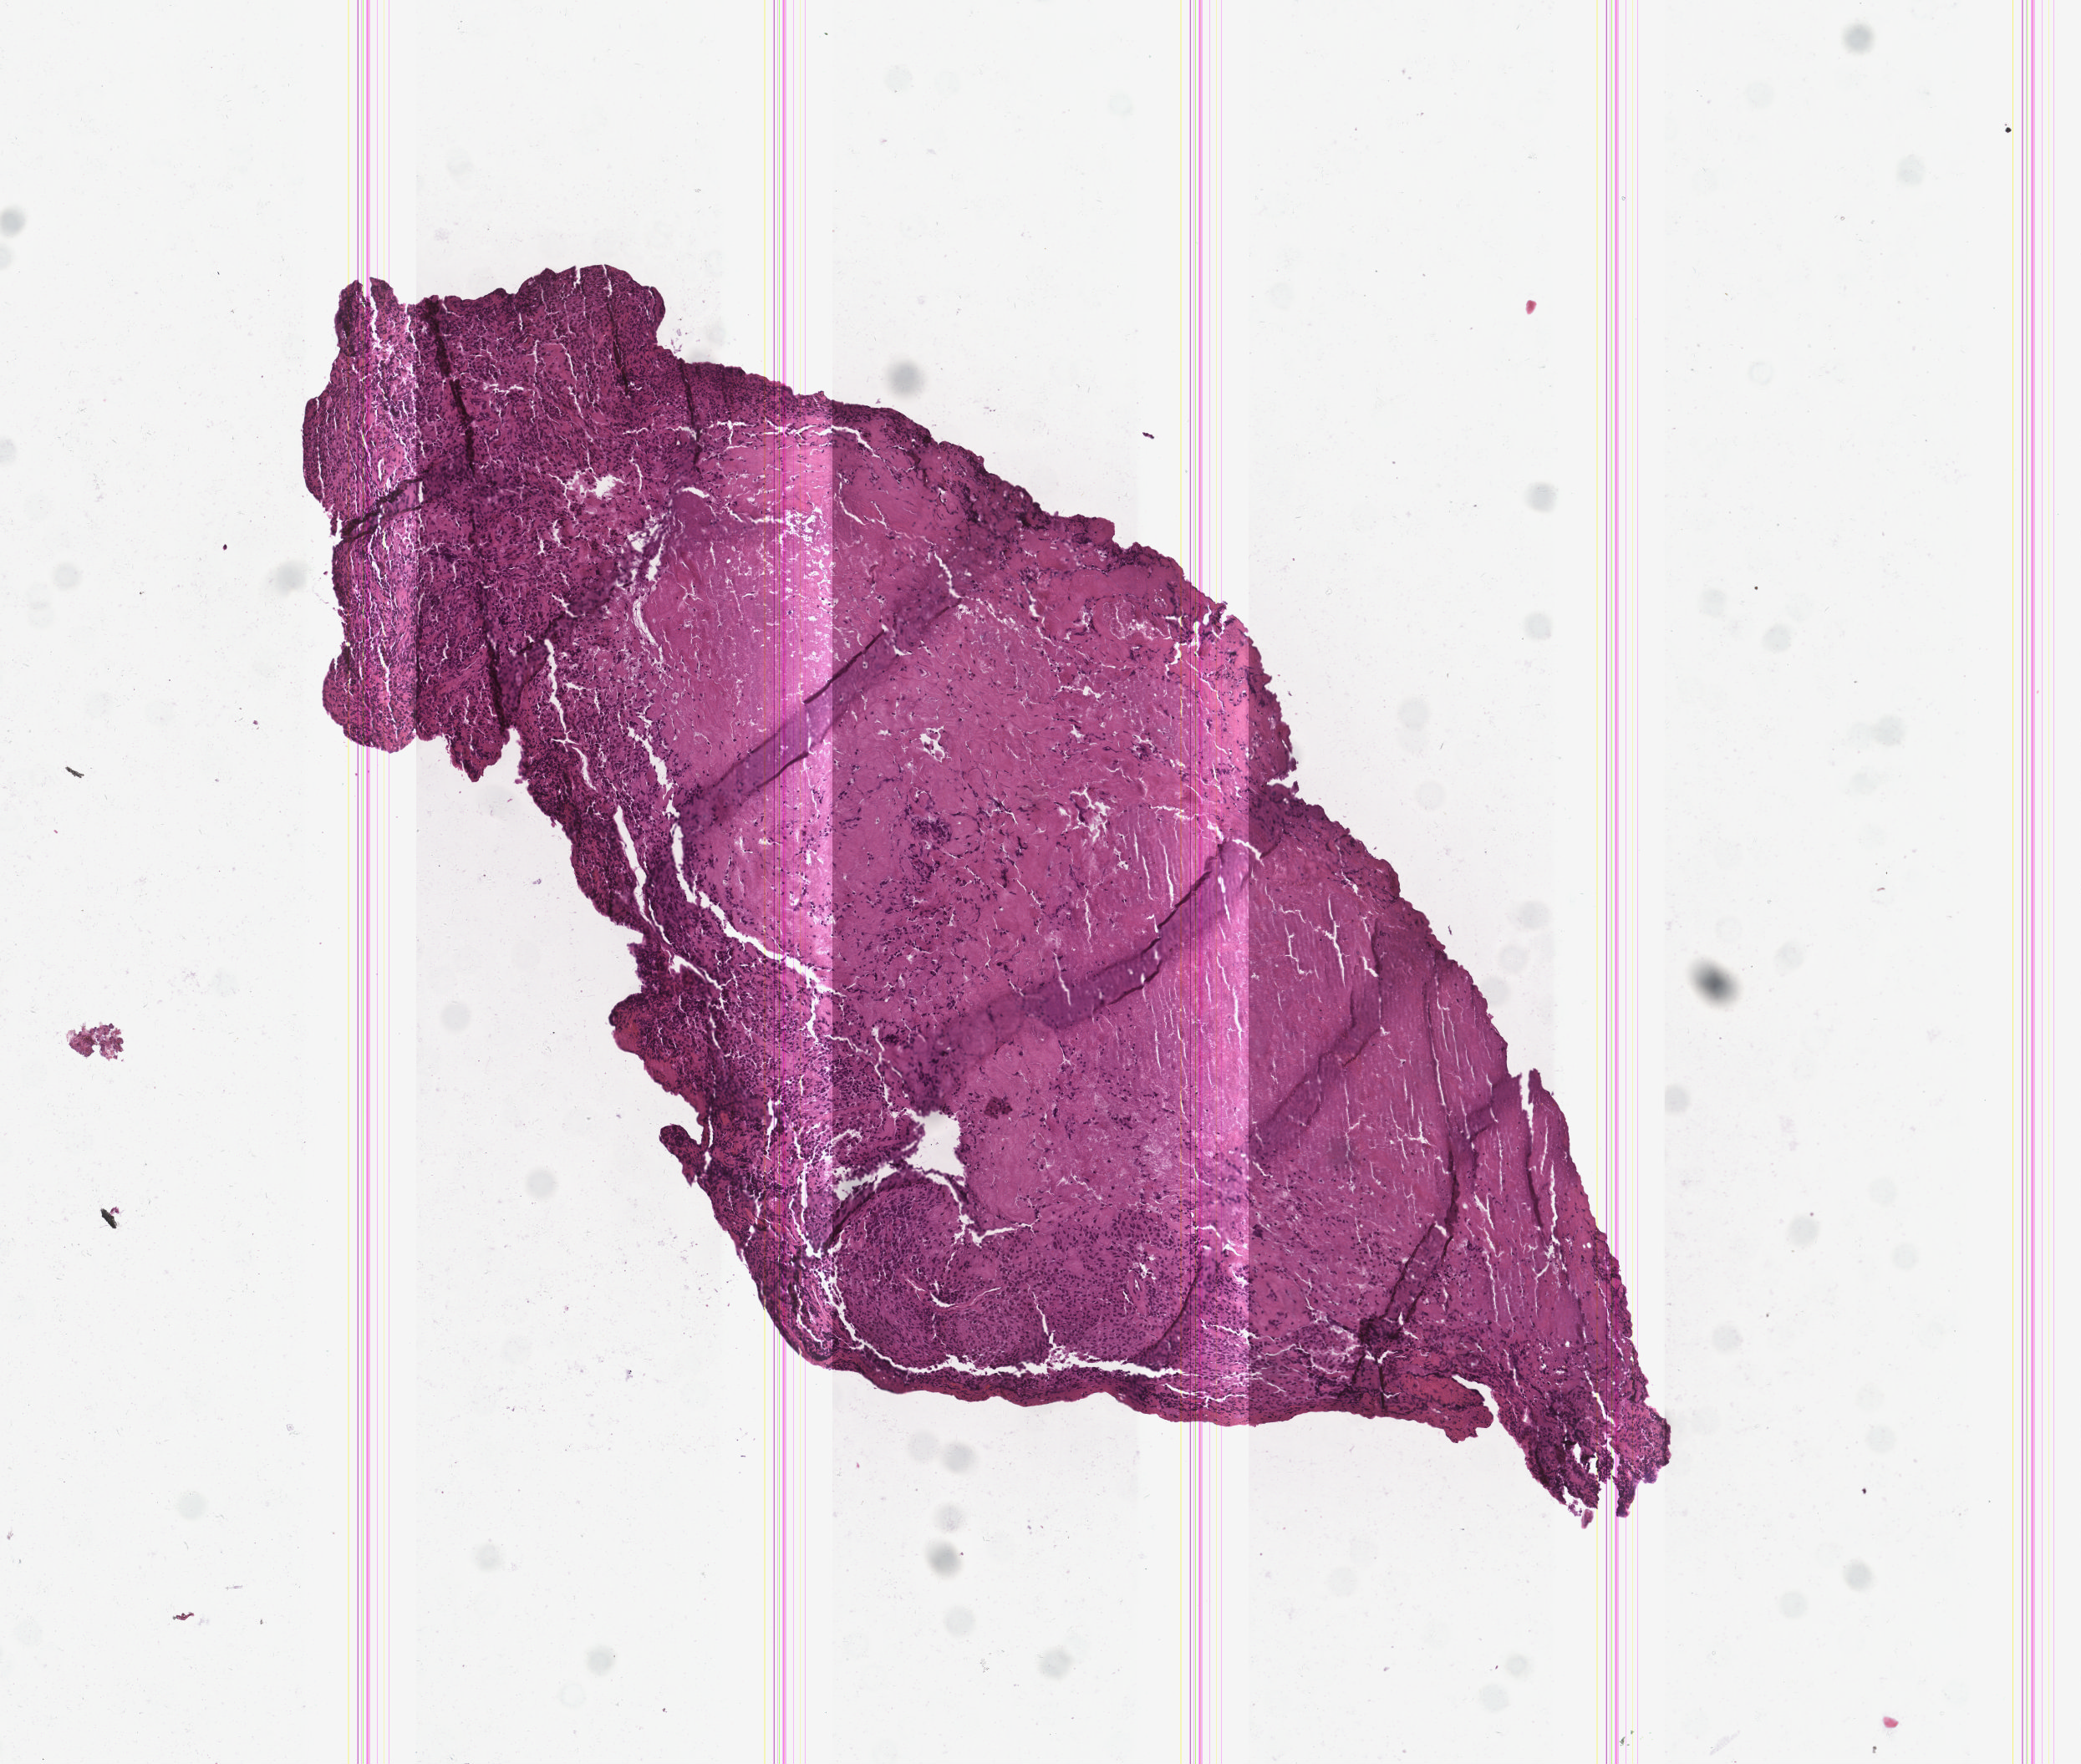
Whole-slide histology image, Hematoxylin and eosin (H&E) stained, shown as a low-resolution overview of the whole scanned area (about 5.0 x 4.3 mm). Brain, tumour tissue. Female, 75 y/o.
- histologic diagnosis: Glioblastoma
- primary tumour site (as recorded): frontal lobe